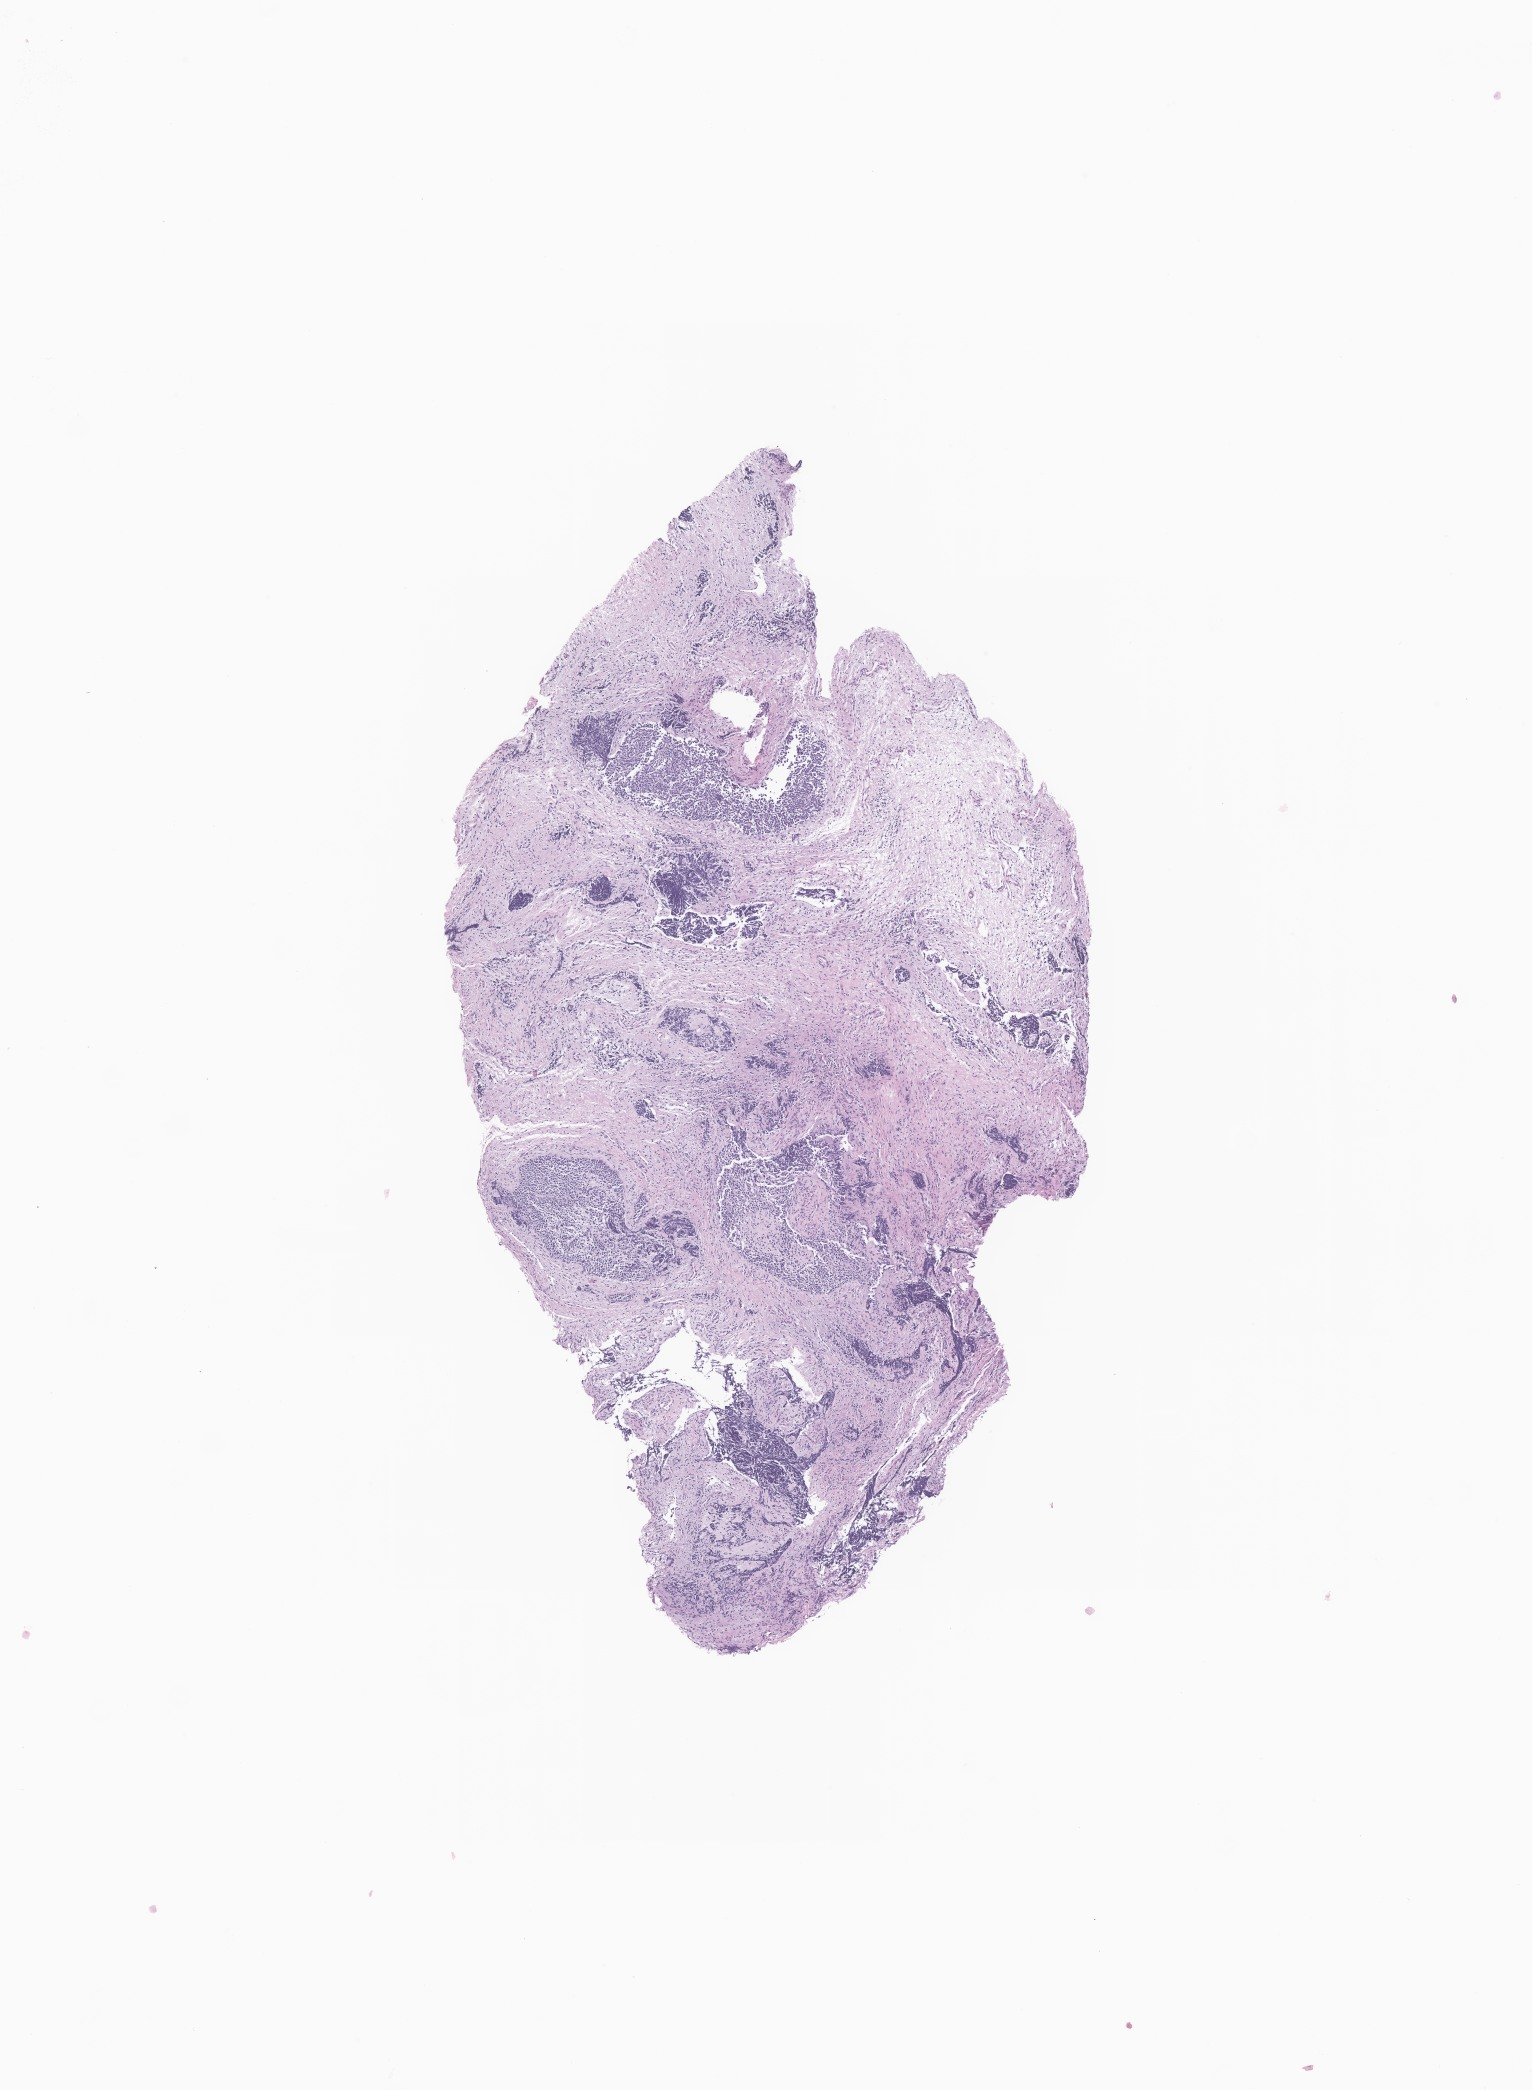
H&E whole-slide image of tumor tissue from the orbit, a low-resolution overview of the entire scanned area, about 6.5 x 8.8 mm; formalin-fixed paraffin-embedded section. Male patient, age 85 days.
Diagnosis (ICD-O-3 morphology term): Sarcoma, NOS.